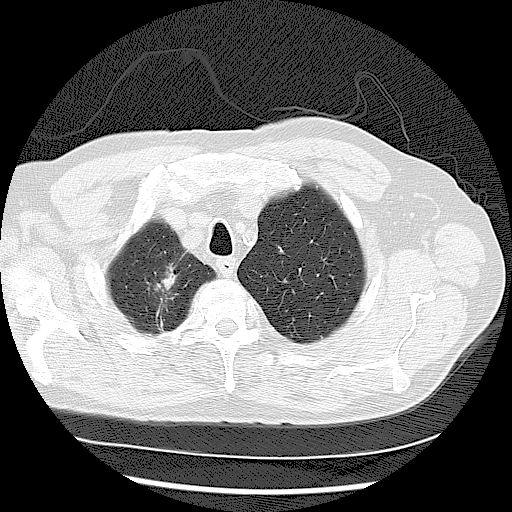
Low-dose screening chest CT, one axial slice; slice 101 of 122 in the series (ordered by position); reconstruction kernel LUNG; lung window (W 1500 / L -600 HU); 2.5 mm slice thickness; 512 × 512 image matrix, field of view 360 × 360 mm.
Outlined on this slice (expert manual segmentation):
- lesion 2 (tumor, upper lobe of right lung): bounding box (x1, y1, x2, y2) in pixels: (154, 263, 178, 292)